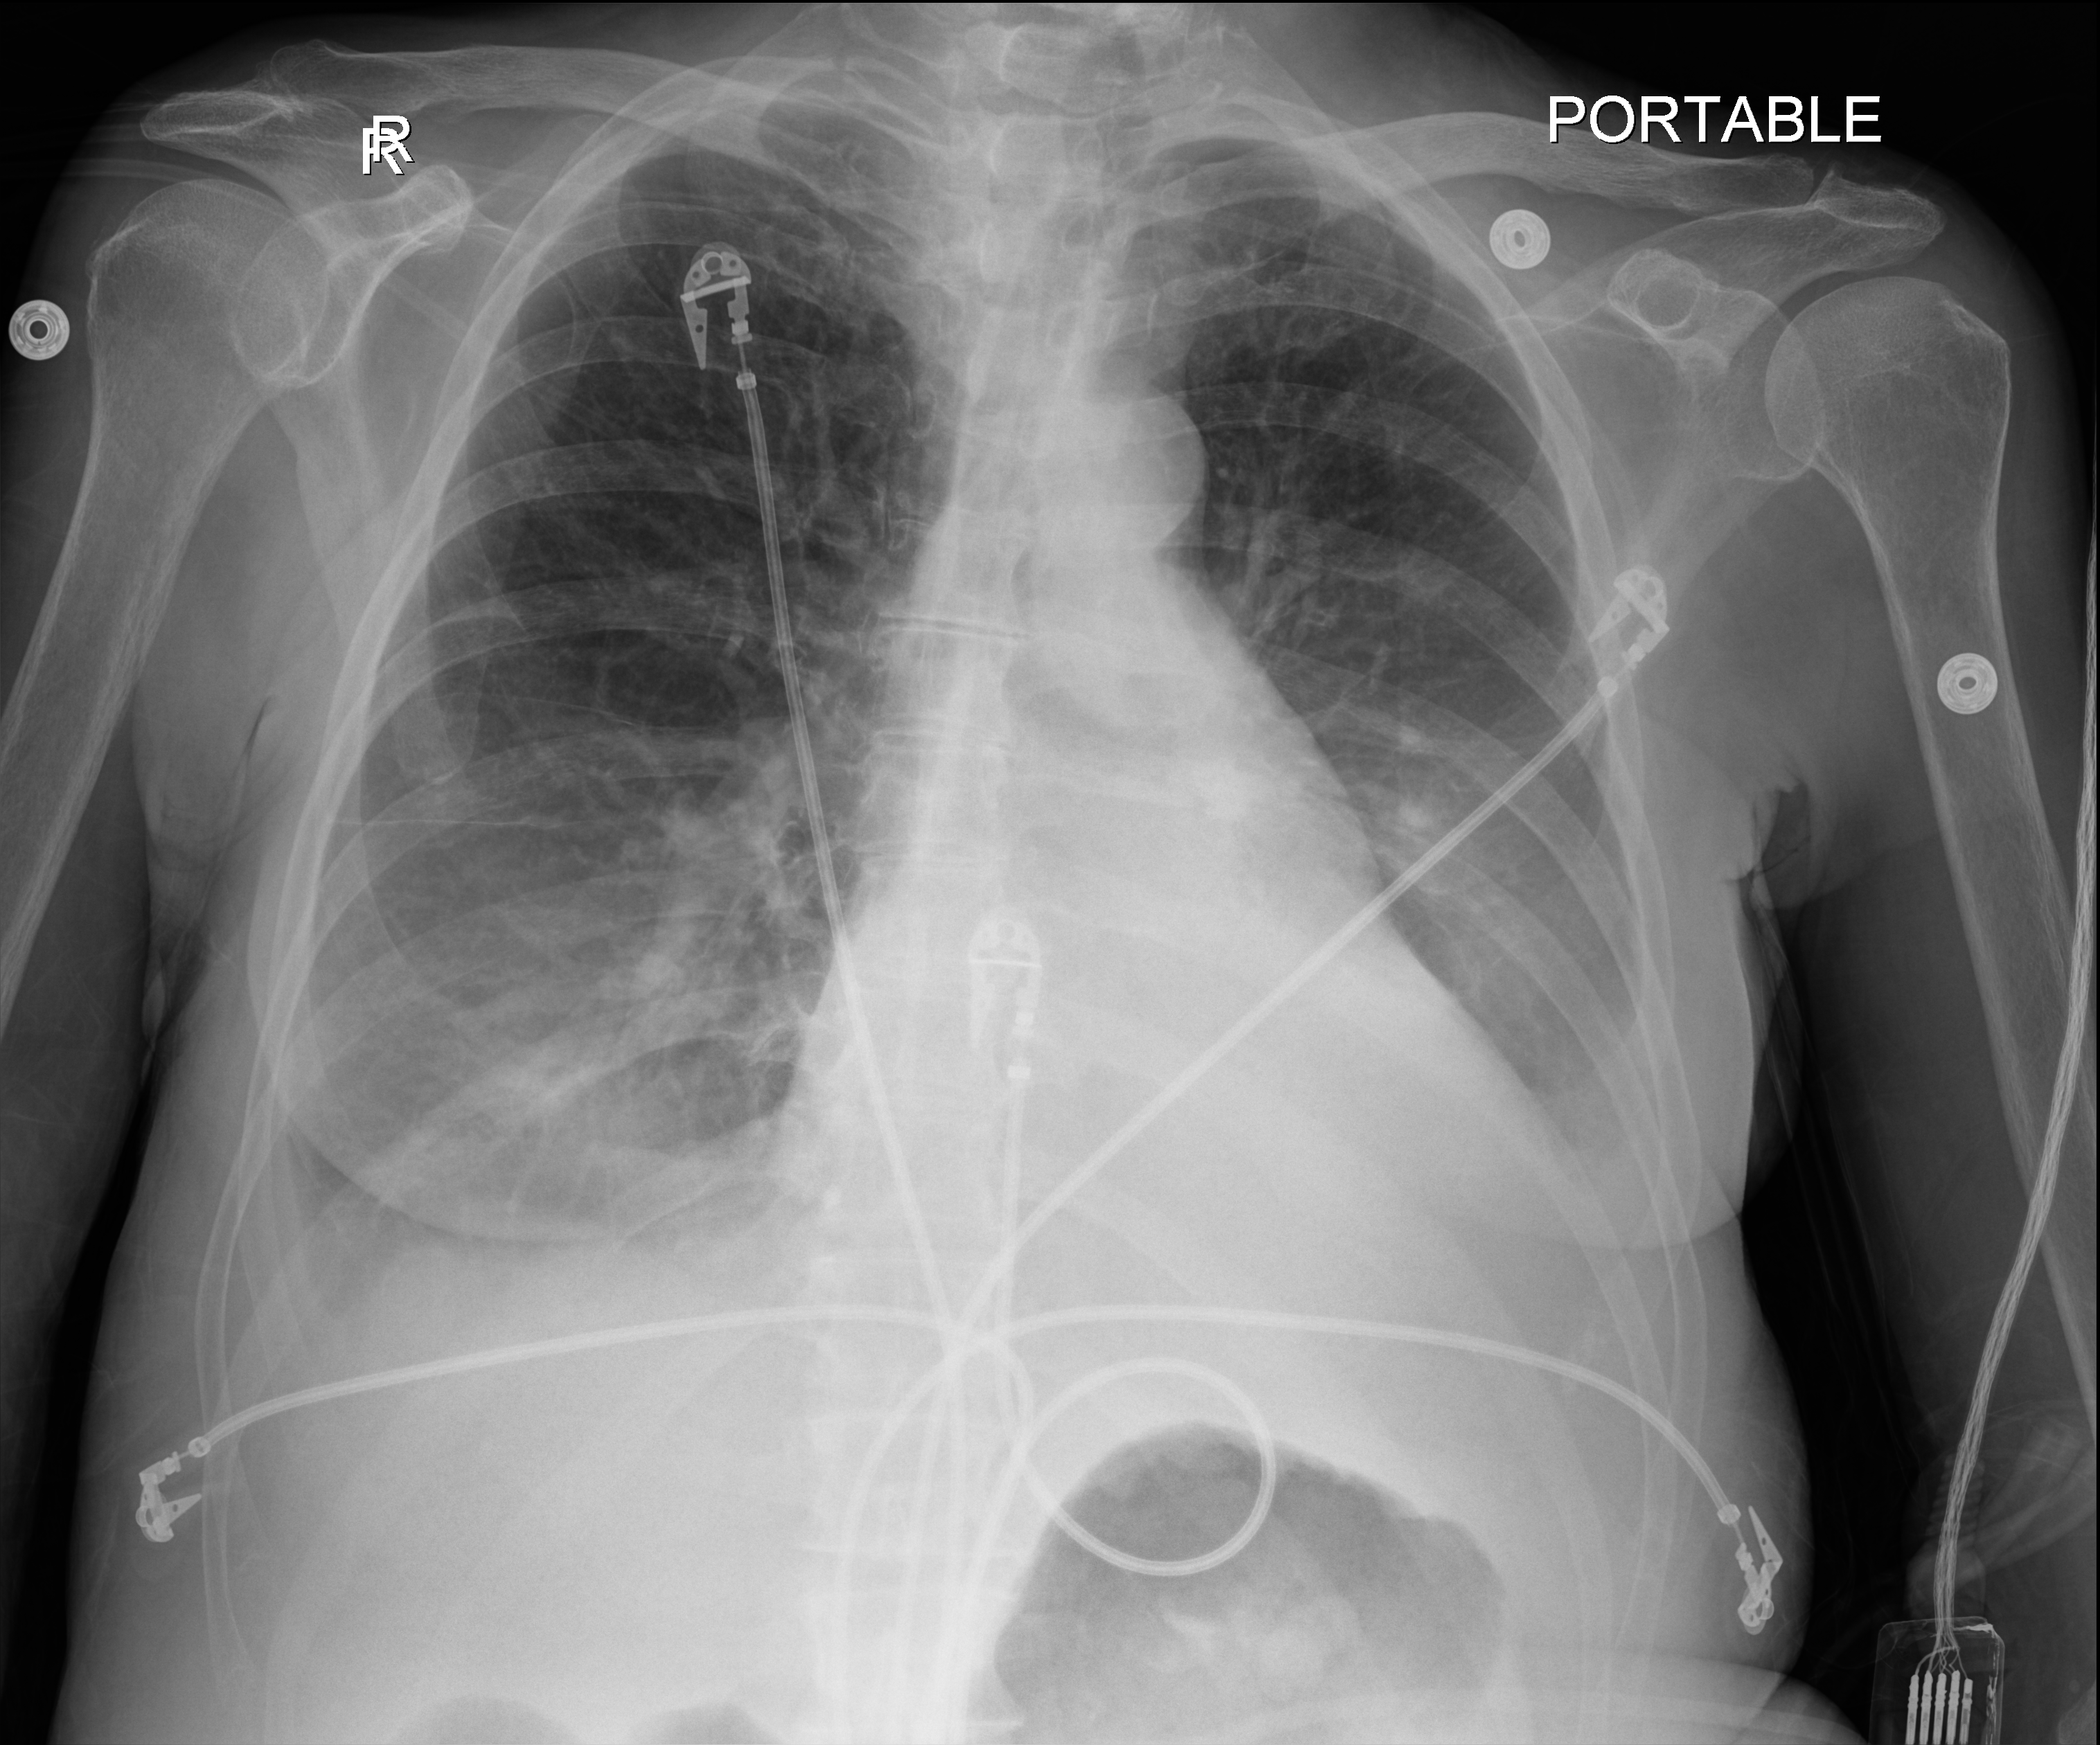
Portable chest radiograph; anteroposterior (AP) projection. Female patient hospitalised with COVID-19, age 60–74 years.
Hospital-stay facts (about this admission, not read from this image; timing relative to this image not recorded):
- length of hospital stay: 38 days
- admitted to intensive care during this hospital stay: yes
- mechanically ventilated during this hospital stay: yes